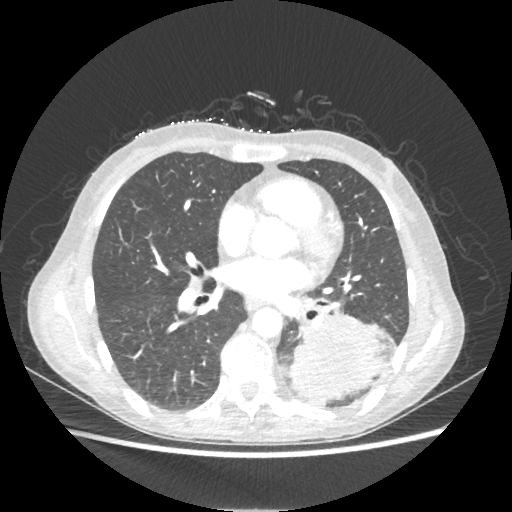
Chest CT, one axial slice. Slice 105 of 221 in the series (ordered by position). Lung window (W 1500 / L -600 HU). 512 × 512 image matrix, field of view 360 × 360 mm. Patient: female, 53 years. From the clinical record (not read from this slice): clinical TNM (as recorded): T3 N0 M0.
Structures marked on this image (bounding box drawn by a radiologist):
- lung tumour (recorded histology: adenocarcinoma): bounding box <290,313,389,401> (left, top, right, bottom; pixels)